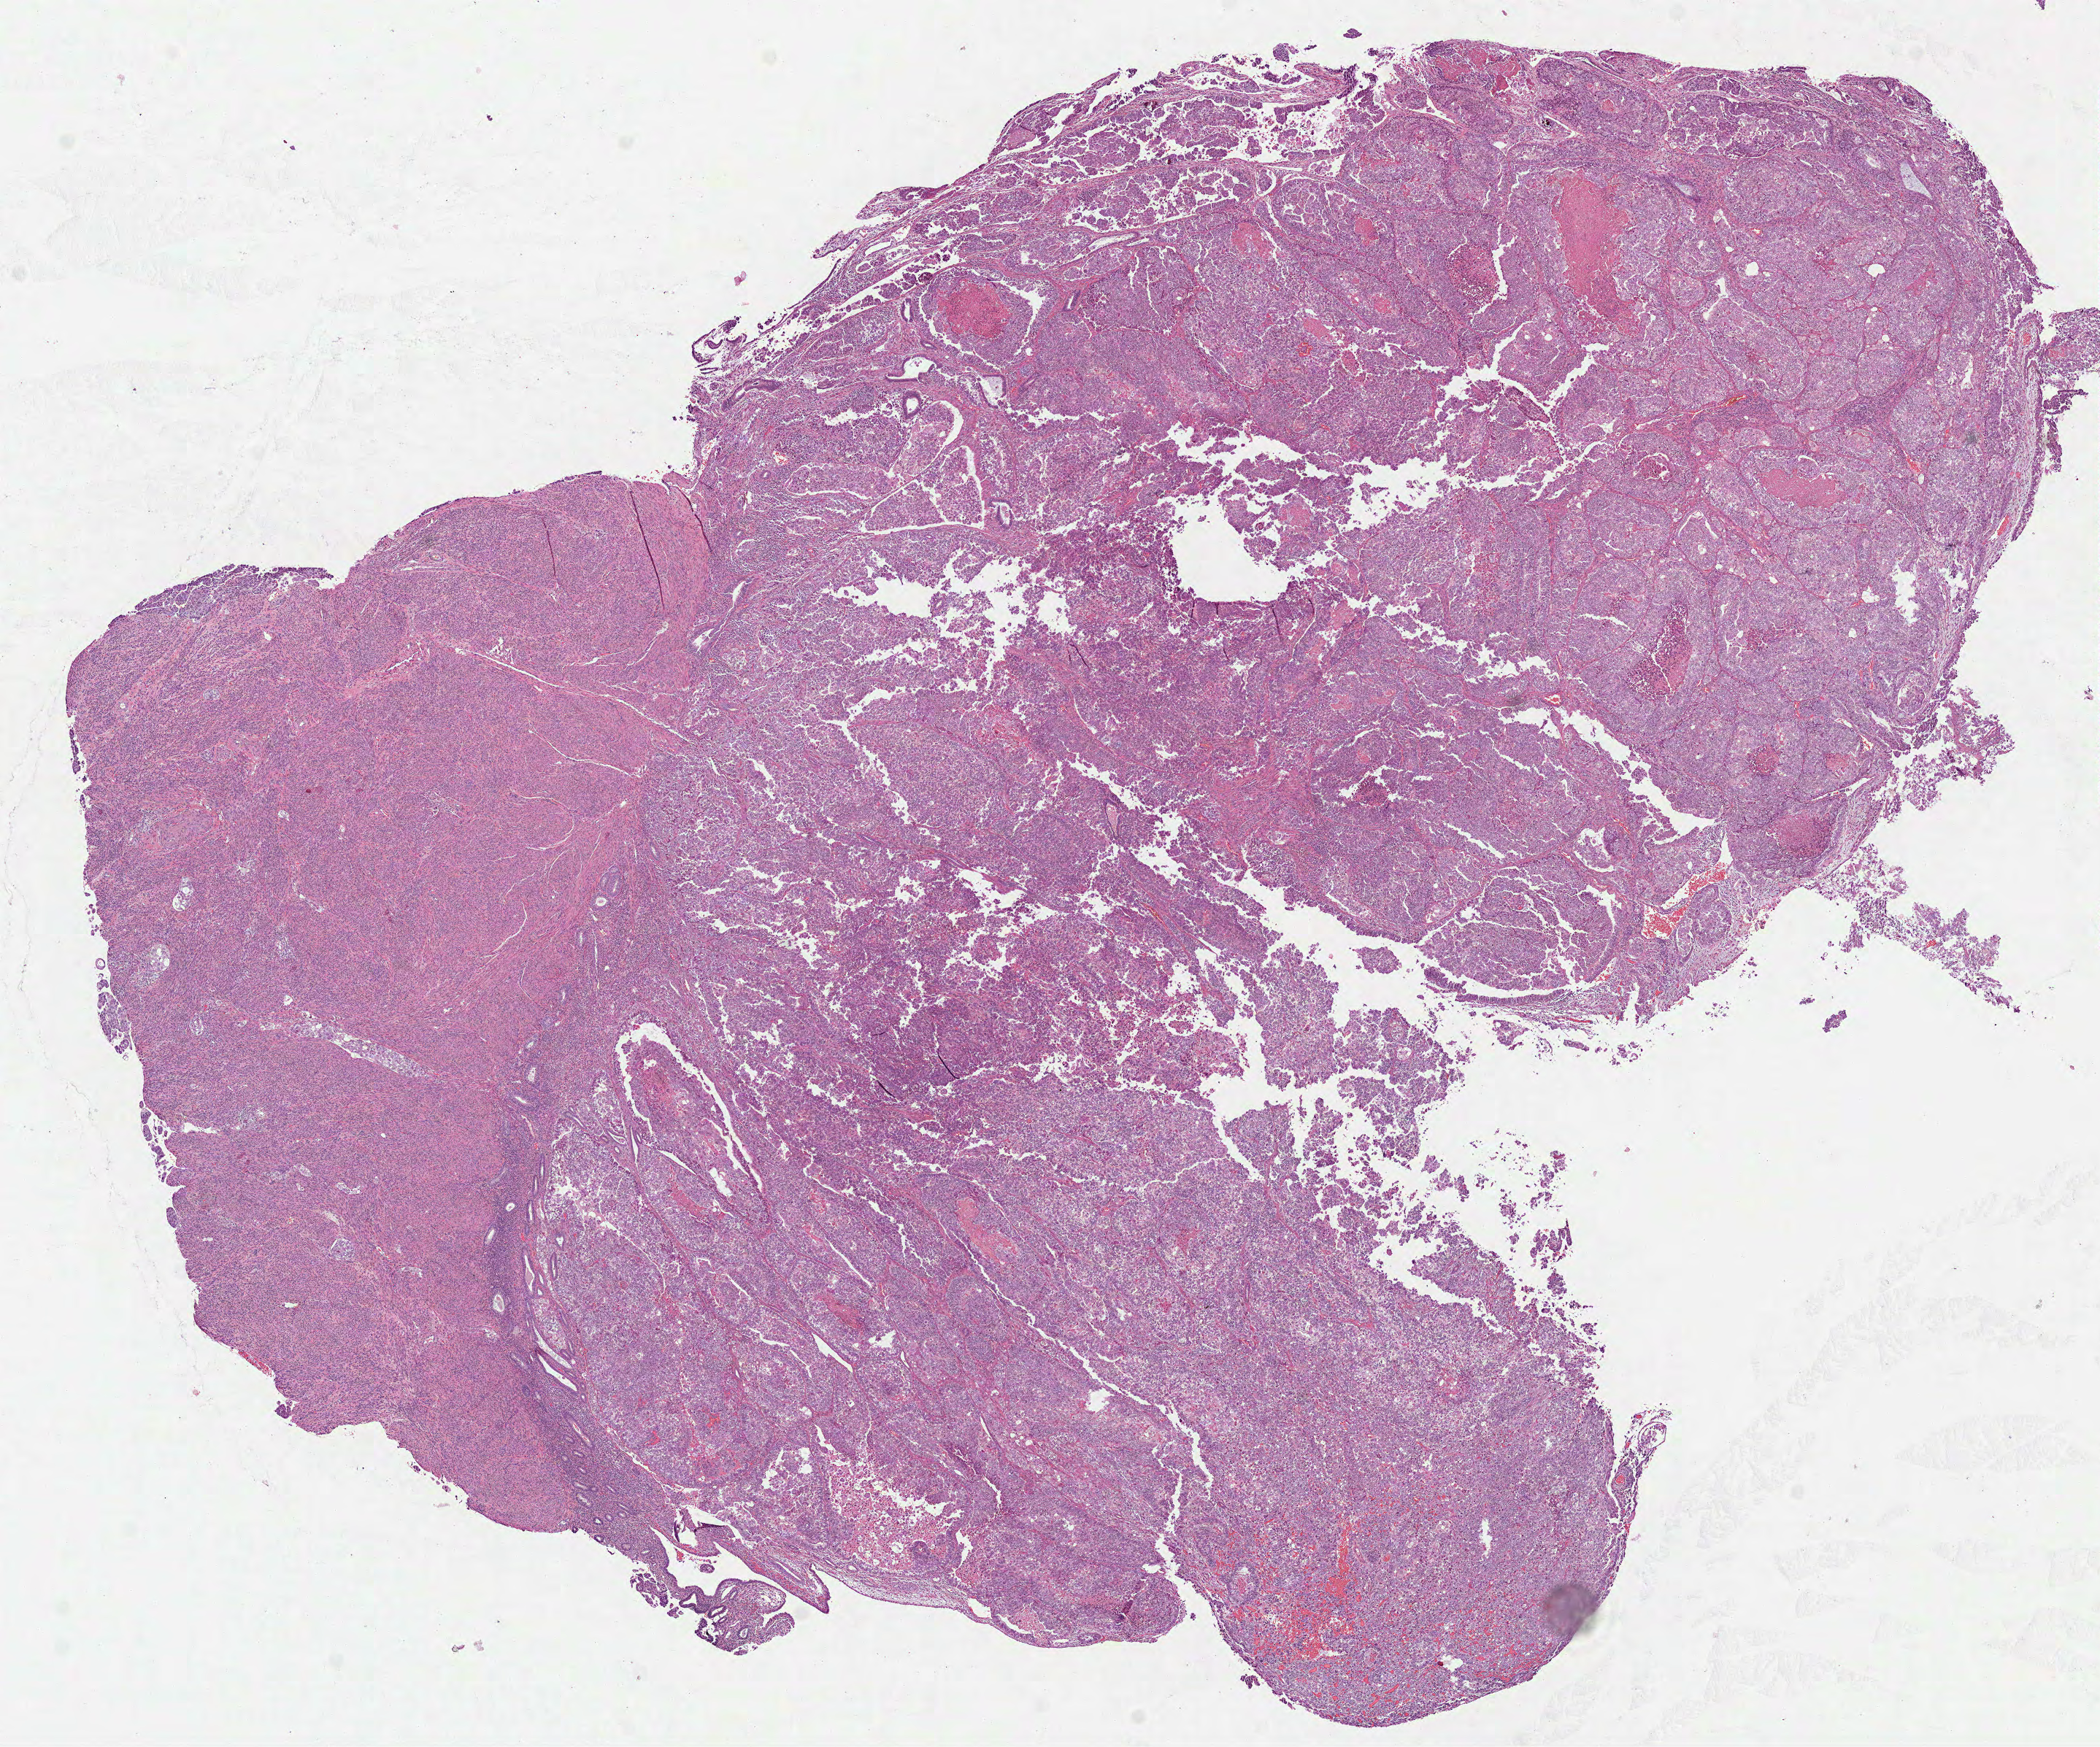
Digitized H&E tissue section (whole slide) — low-resolution overview of the scanned area, about 11.6 x 9.7 mm; formalin-fixed paraffin-embedded (FFPE) diagnostic section; sample: primary tumour, uterus. Female patient; age at initial diagnosis 65 years. Histologic grade: G3 (poorly differentiated).
• FIGO stage: IIIC2
• histologic diagnosis: Papillary serous cystadenocarcinoma (endometrium)